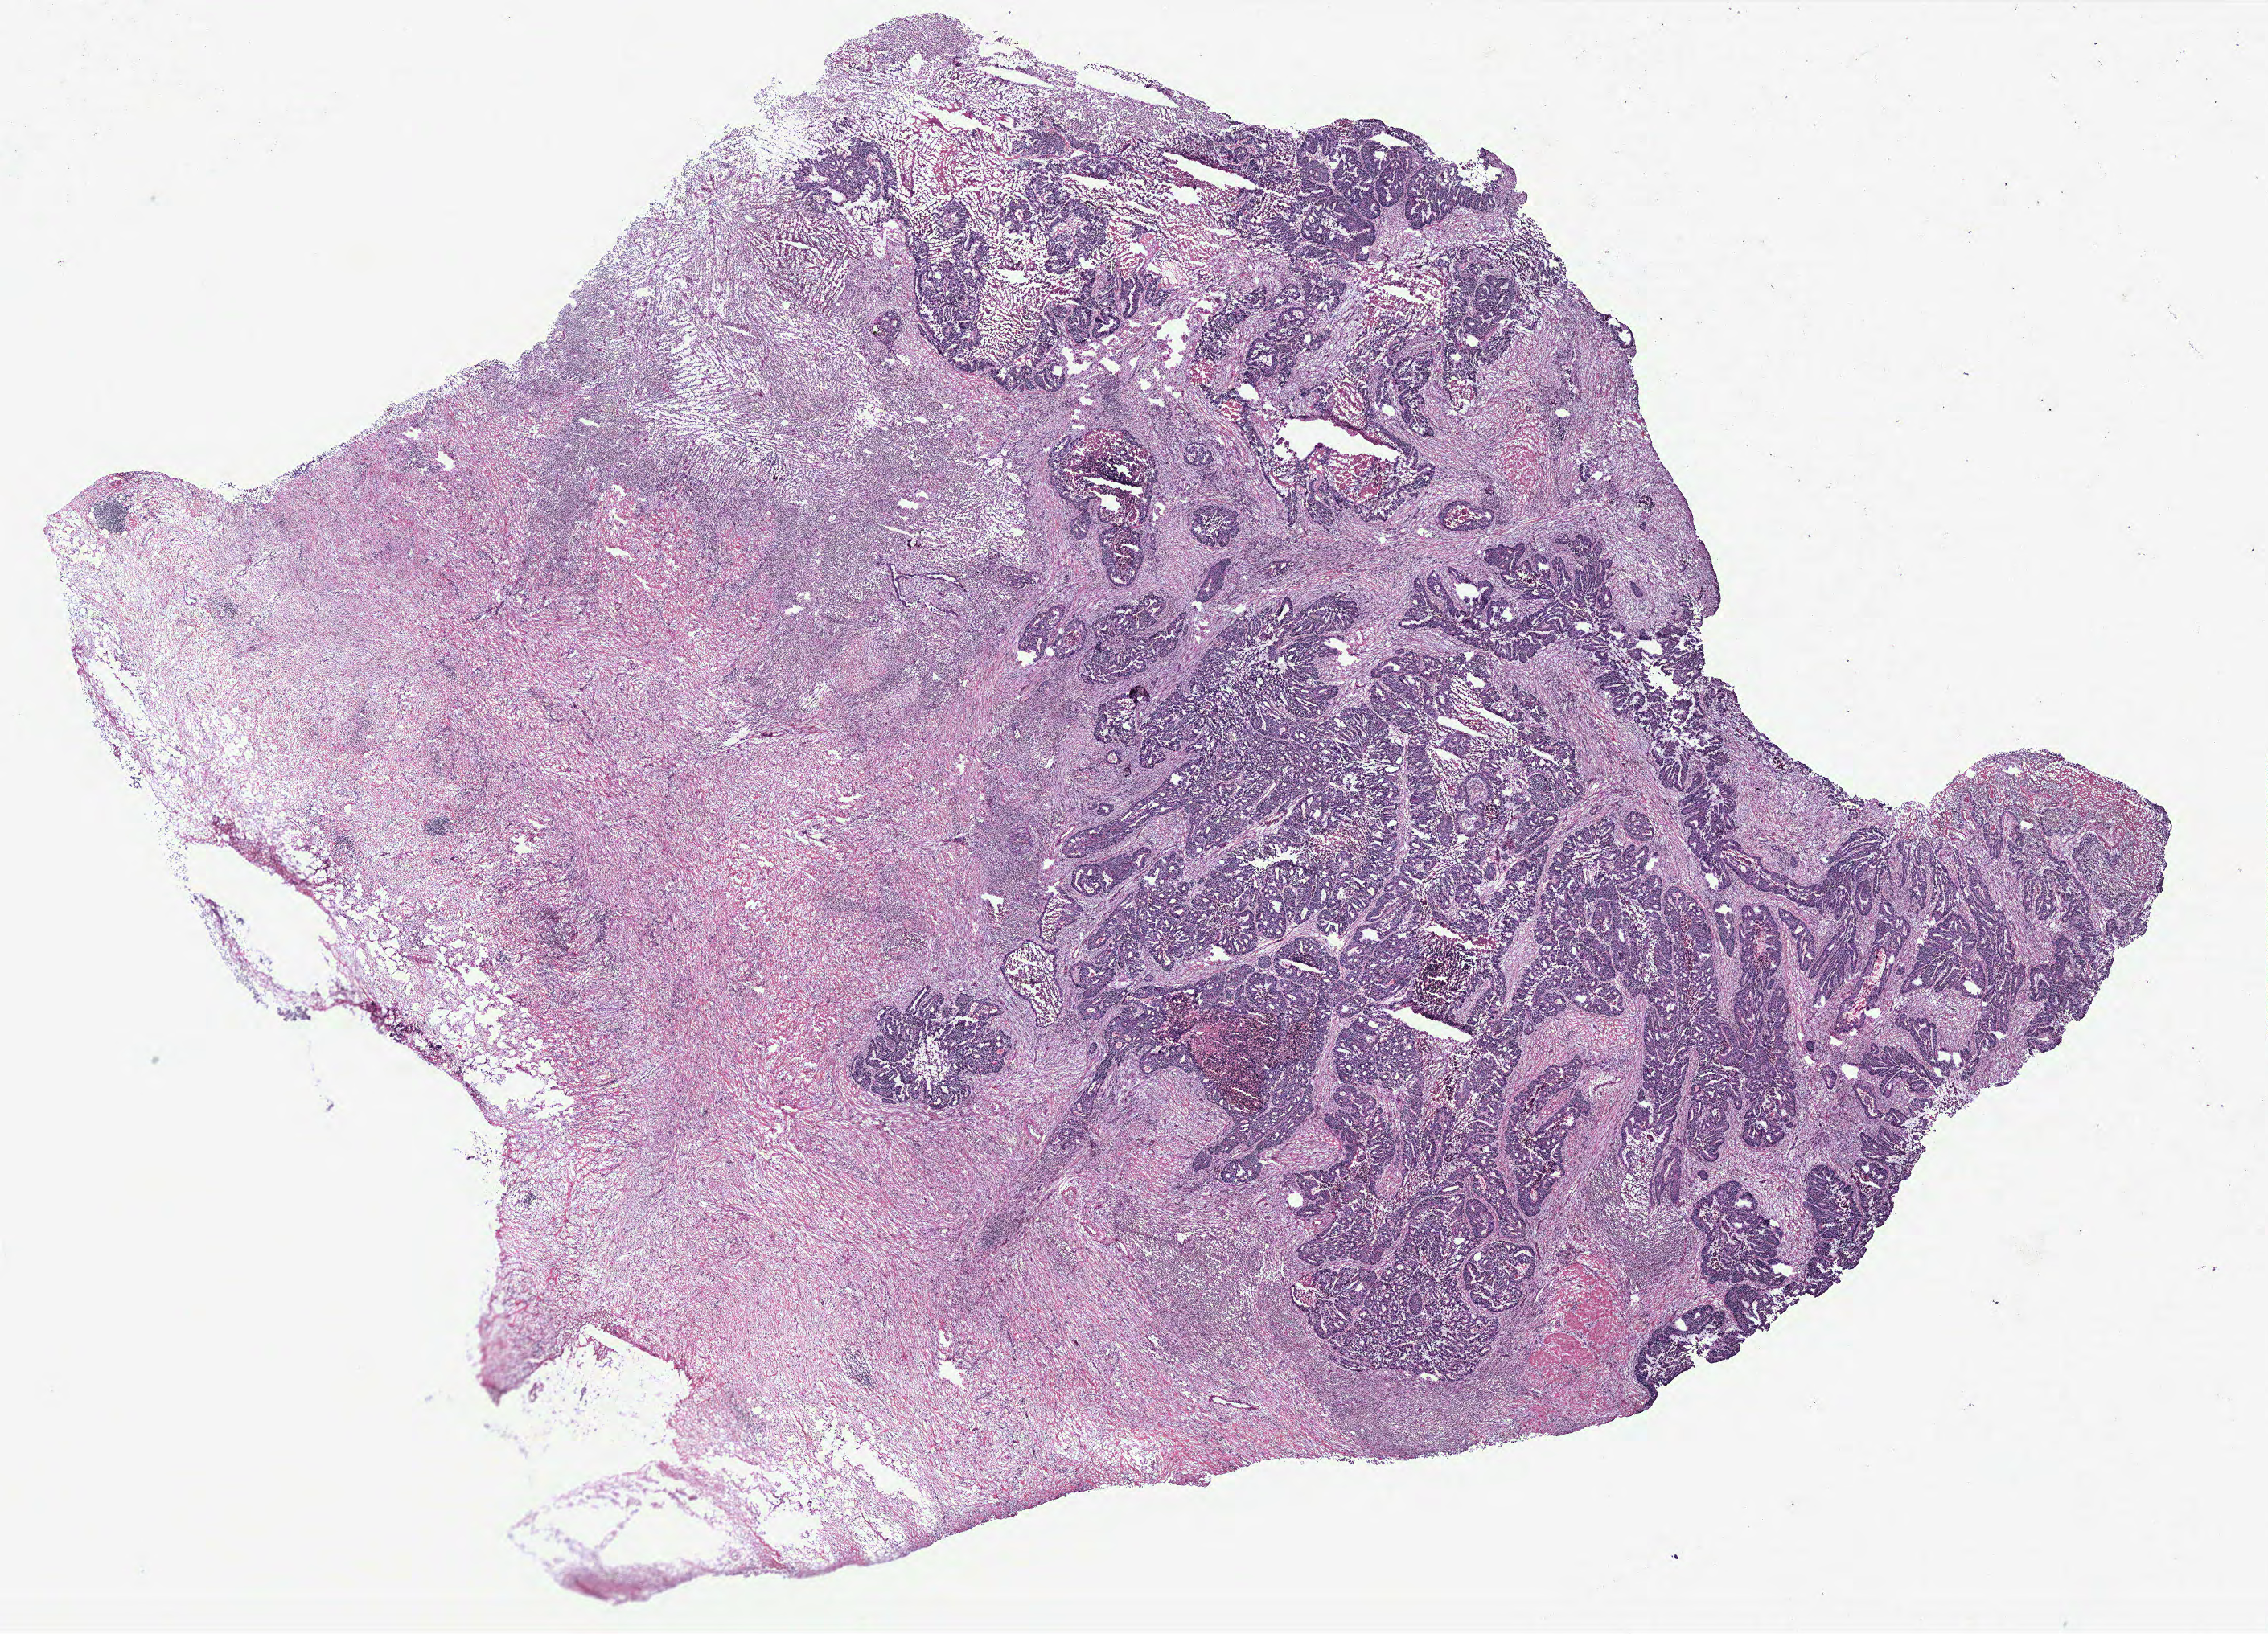
H&E-stained whole-slide image, whole scanned area (about 22.6 x 16.3 mm, from a 40x scan) shown as a low-resolution overview; colon, tumour tissue. Patient: male, age 65 years.
Histologic diagnosis: Adenocarcinoma, NOS. Primary tumour site (as recorded): colon. AJCC pathologic stage: IIA.